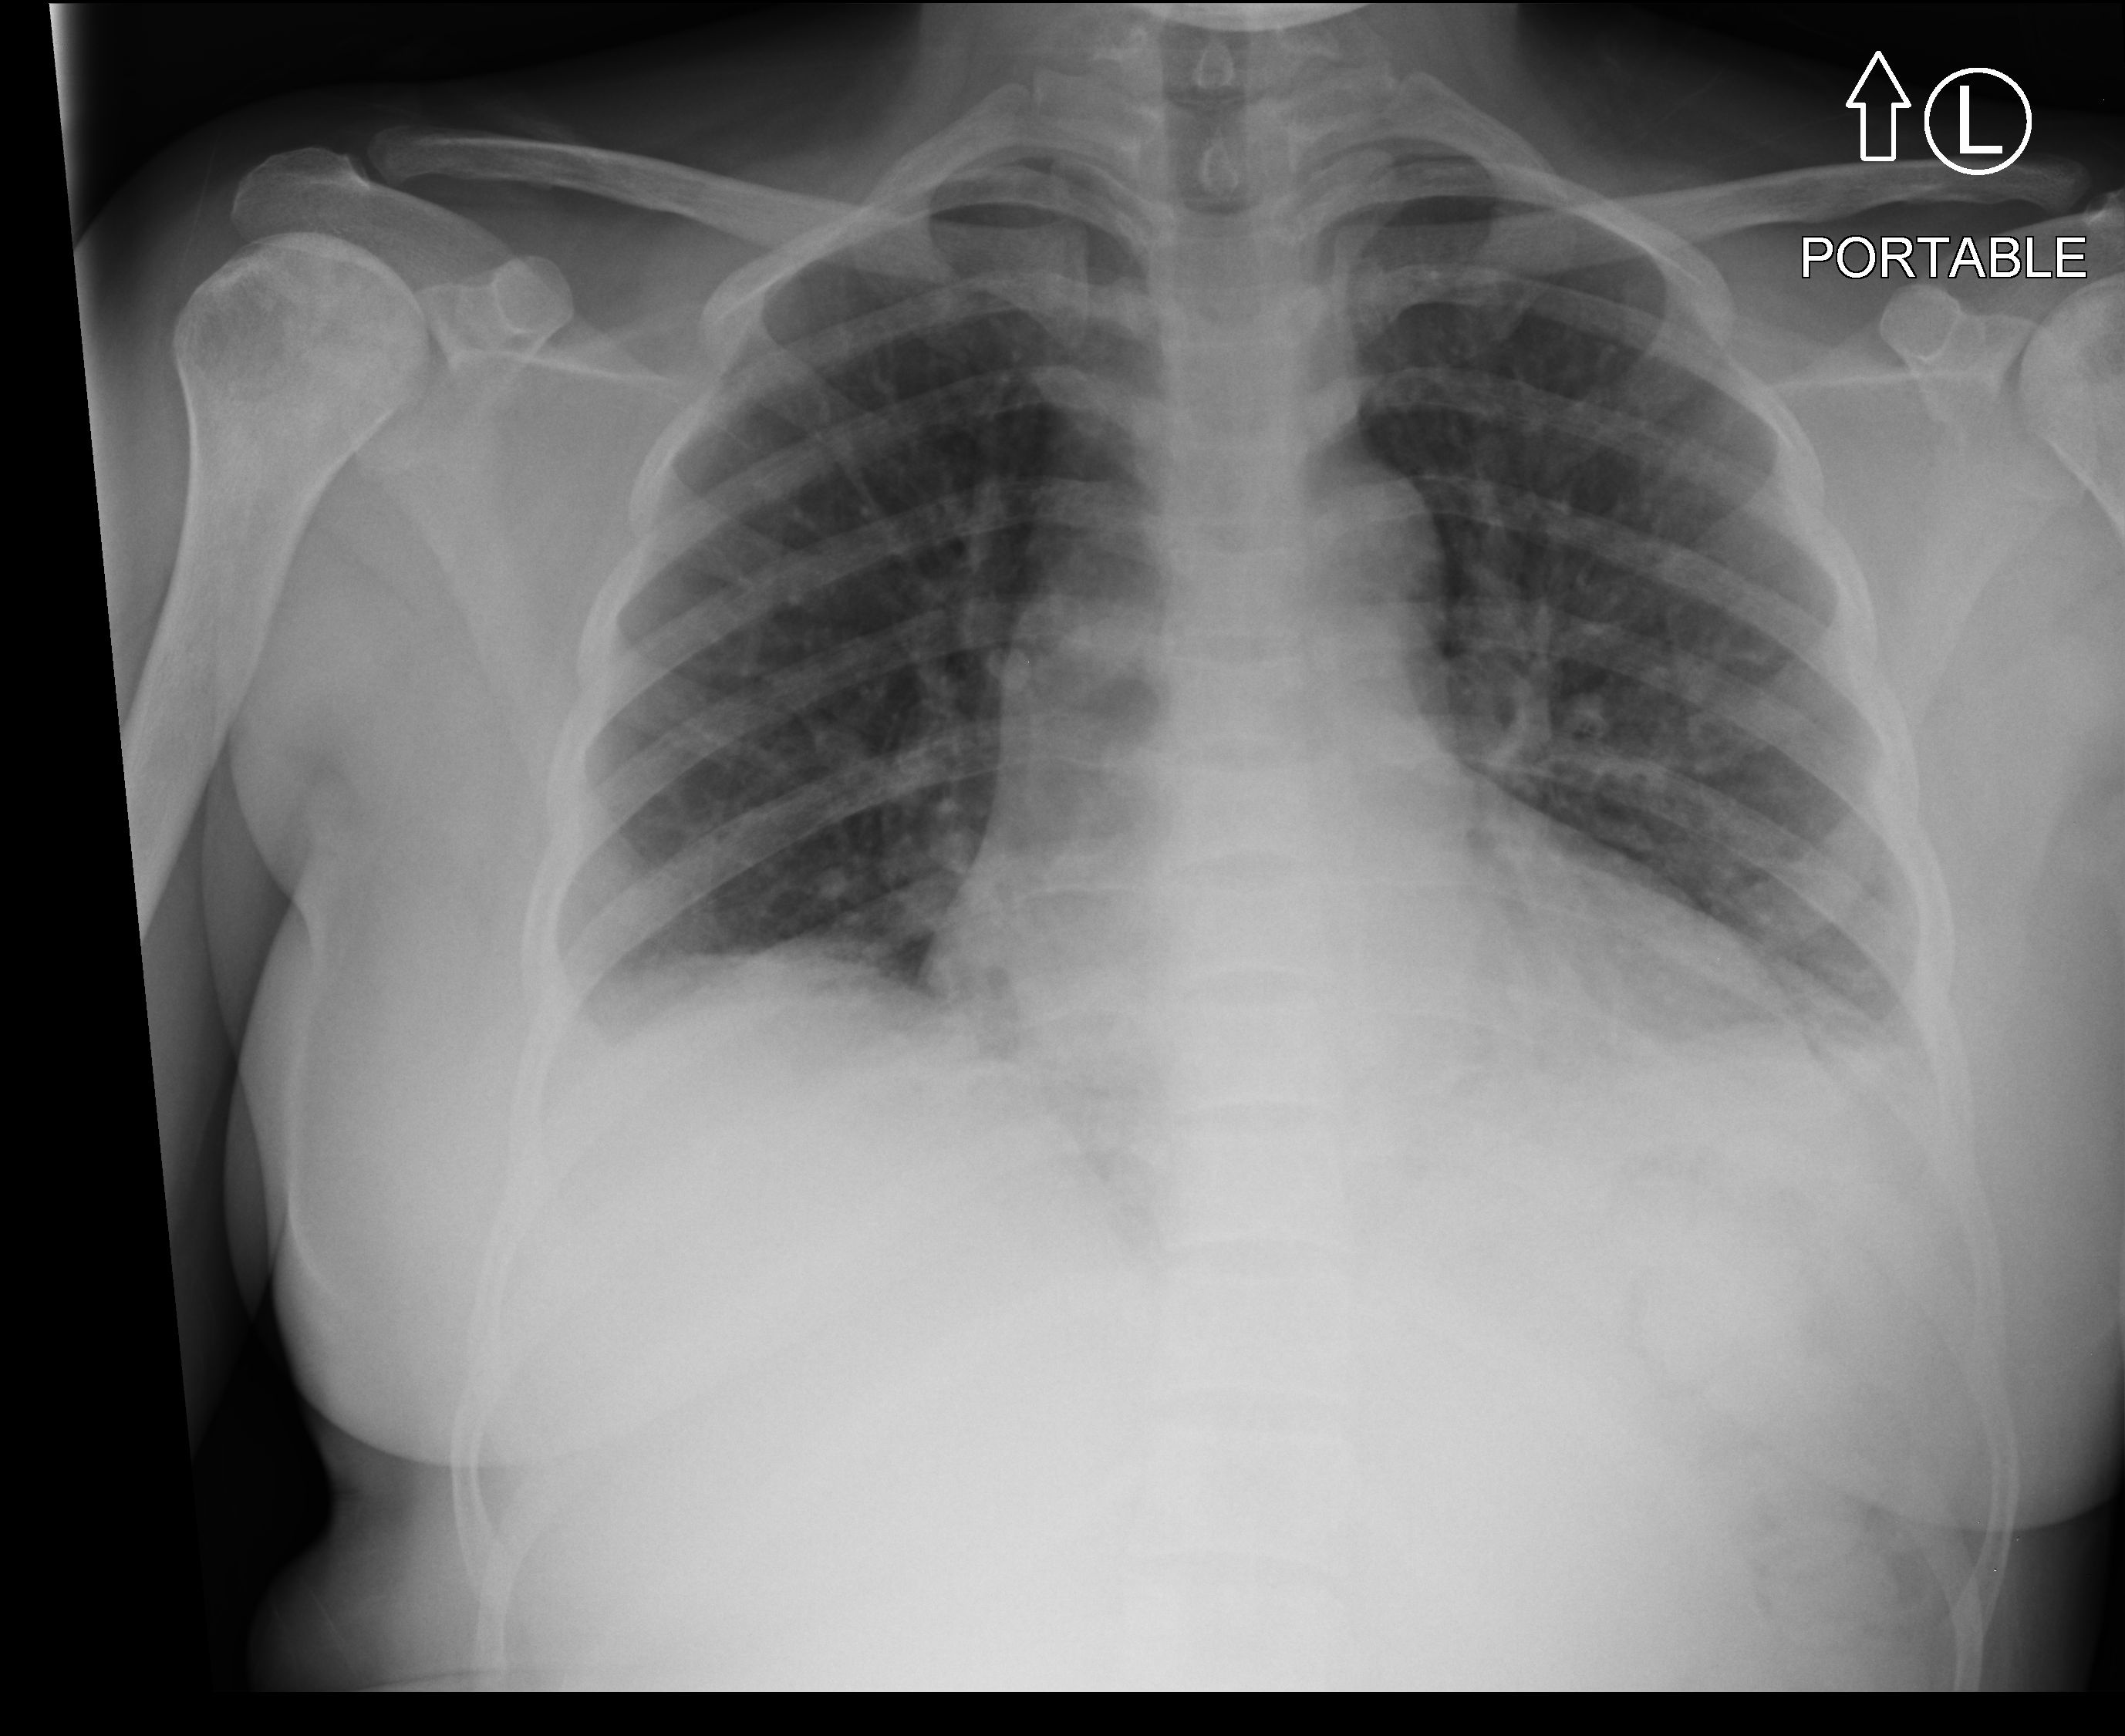
Portable chest radiograph, anteroposterior (AP) projection. Patient hospitalised with COVID-19; female, aged 18–59 years.
Admission-level facts for this patient (not findings on this image; timing relative to this image not recorded): length of hospital stay: 9 days; diabetes (admission record): no; other chronic lung disease (admission record): no.